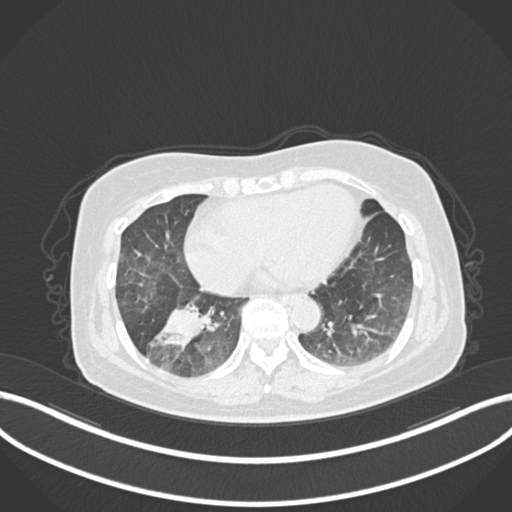
Chest CT, one axial slice; position 43 of 222 along the scan axis; lung window (W 1500 / L -600 HU); 512 × 512 image matrix, field of view 400 × 400 mm. Patient: female, 67 years. From the clinical record (not read from this slice): clinical TNM (as recorded): T1c N1 M0; histopathological grade: G2-3.
Annotated regions visible in this slice (rectangle marked by the reading radiologist):
- lung tumour (recorded histology: adenocarcinoma): bounding box (x1, y1, x2, y2) in pixels: (147, 298, 219, 355)